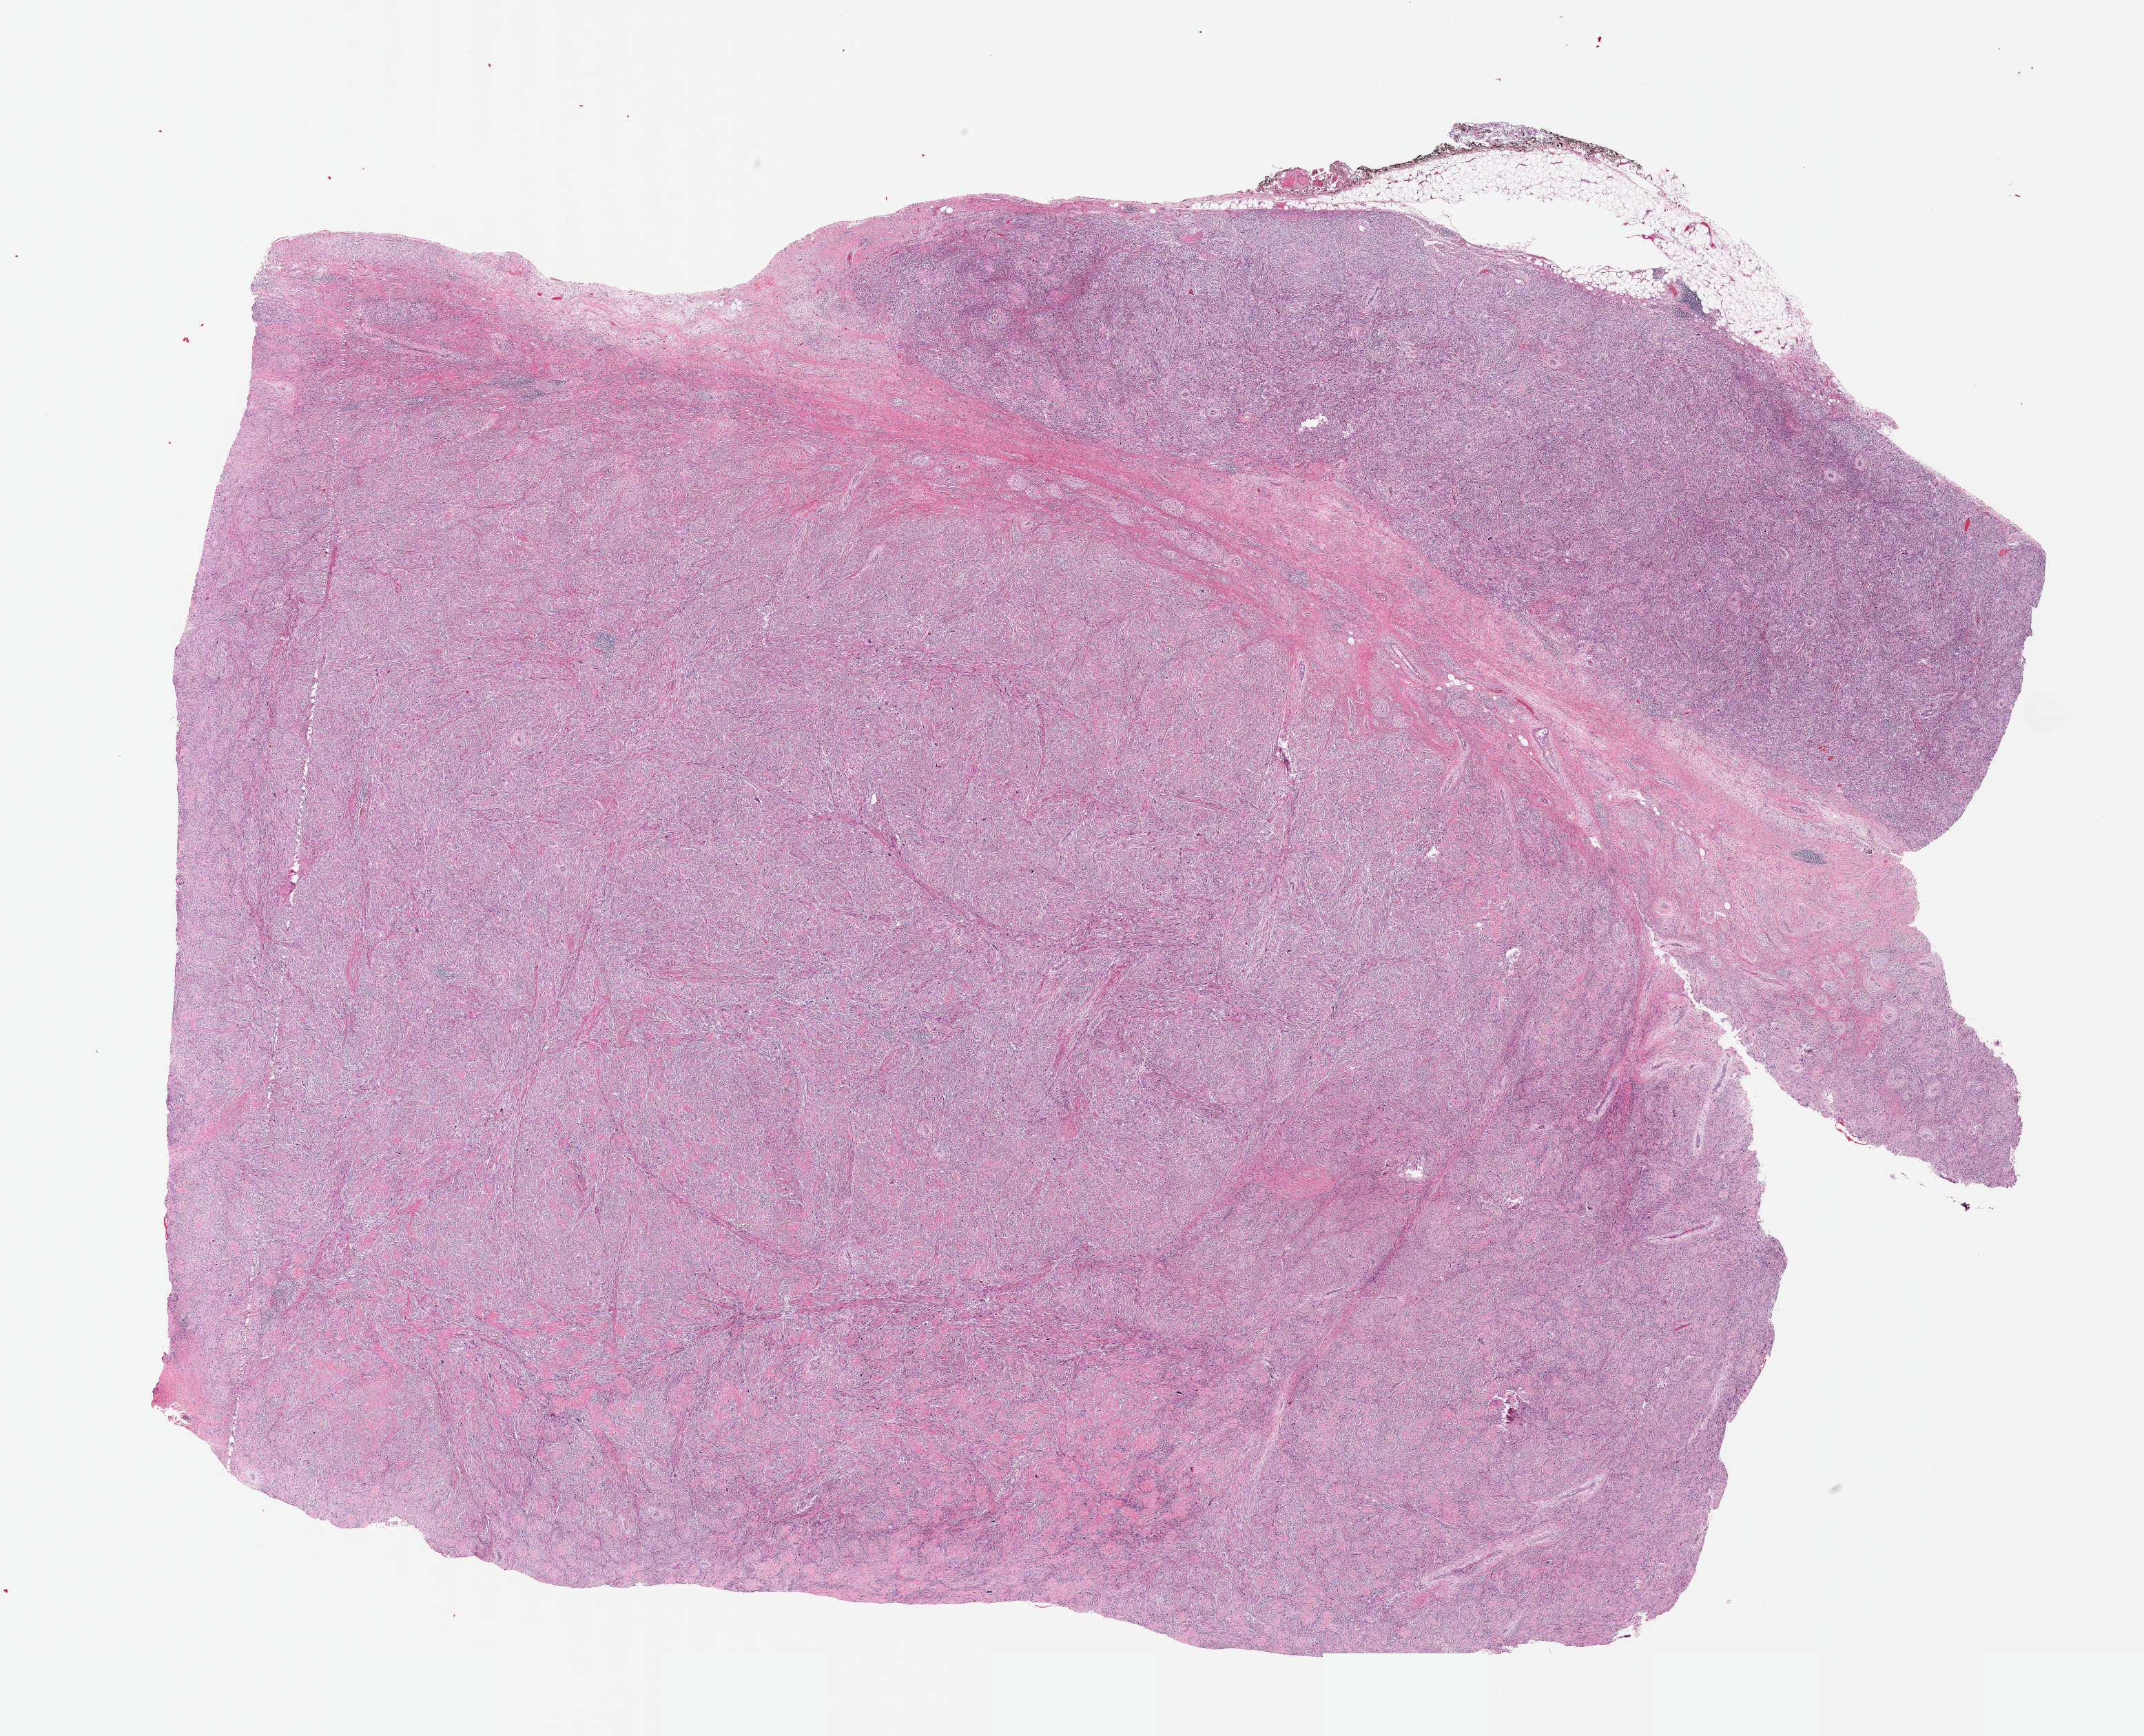
Whole-slide histology image, Hematoxylin and eosin (H&E) stained — whole scanned area (about 25.1 x 20.4 mm, slide scanned at 40x) shown as a low-resolution overview; FFPE section; retroperitoneum and peritoneum, primary tumour sample. Male, age 53 years at initial diagnosis.
* diagnosis: Dedifferentiated liposarcoma